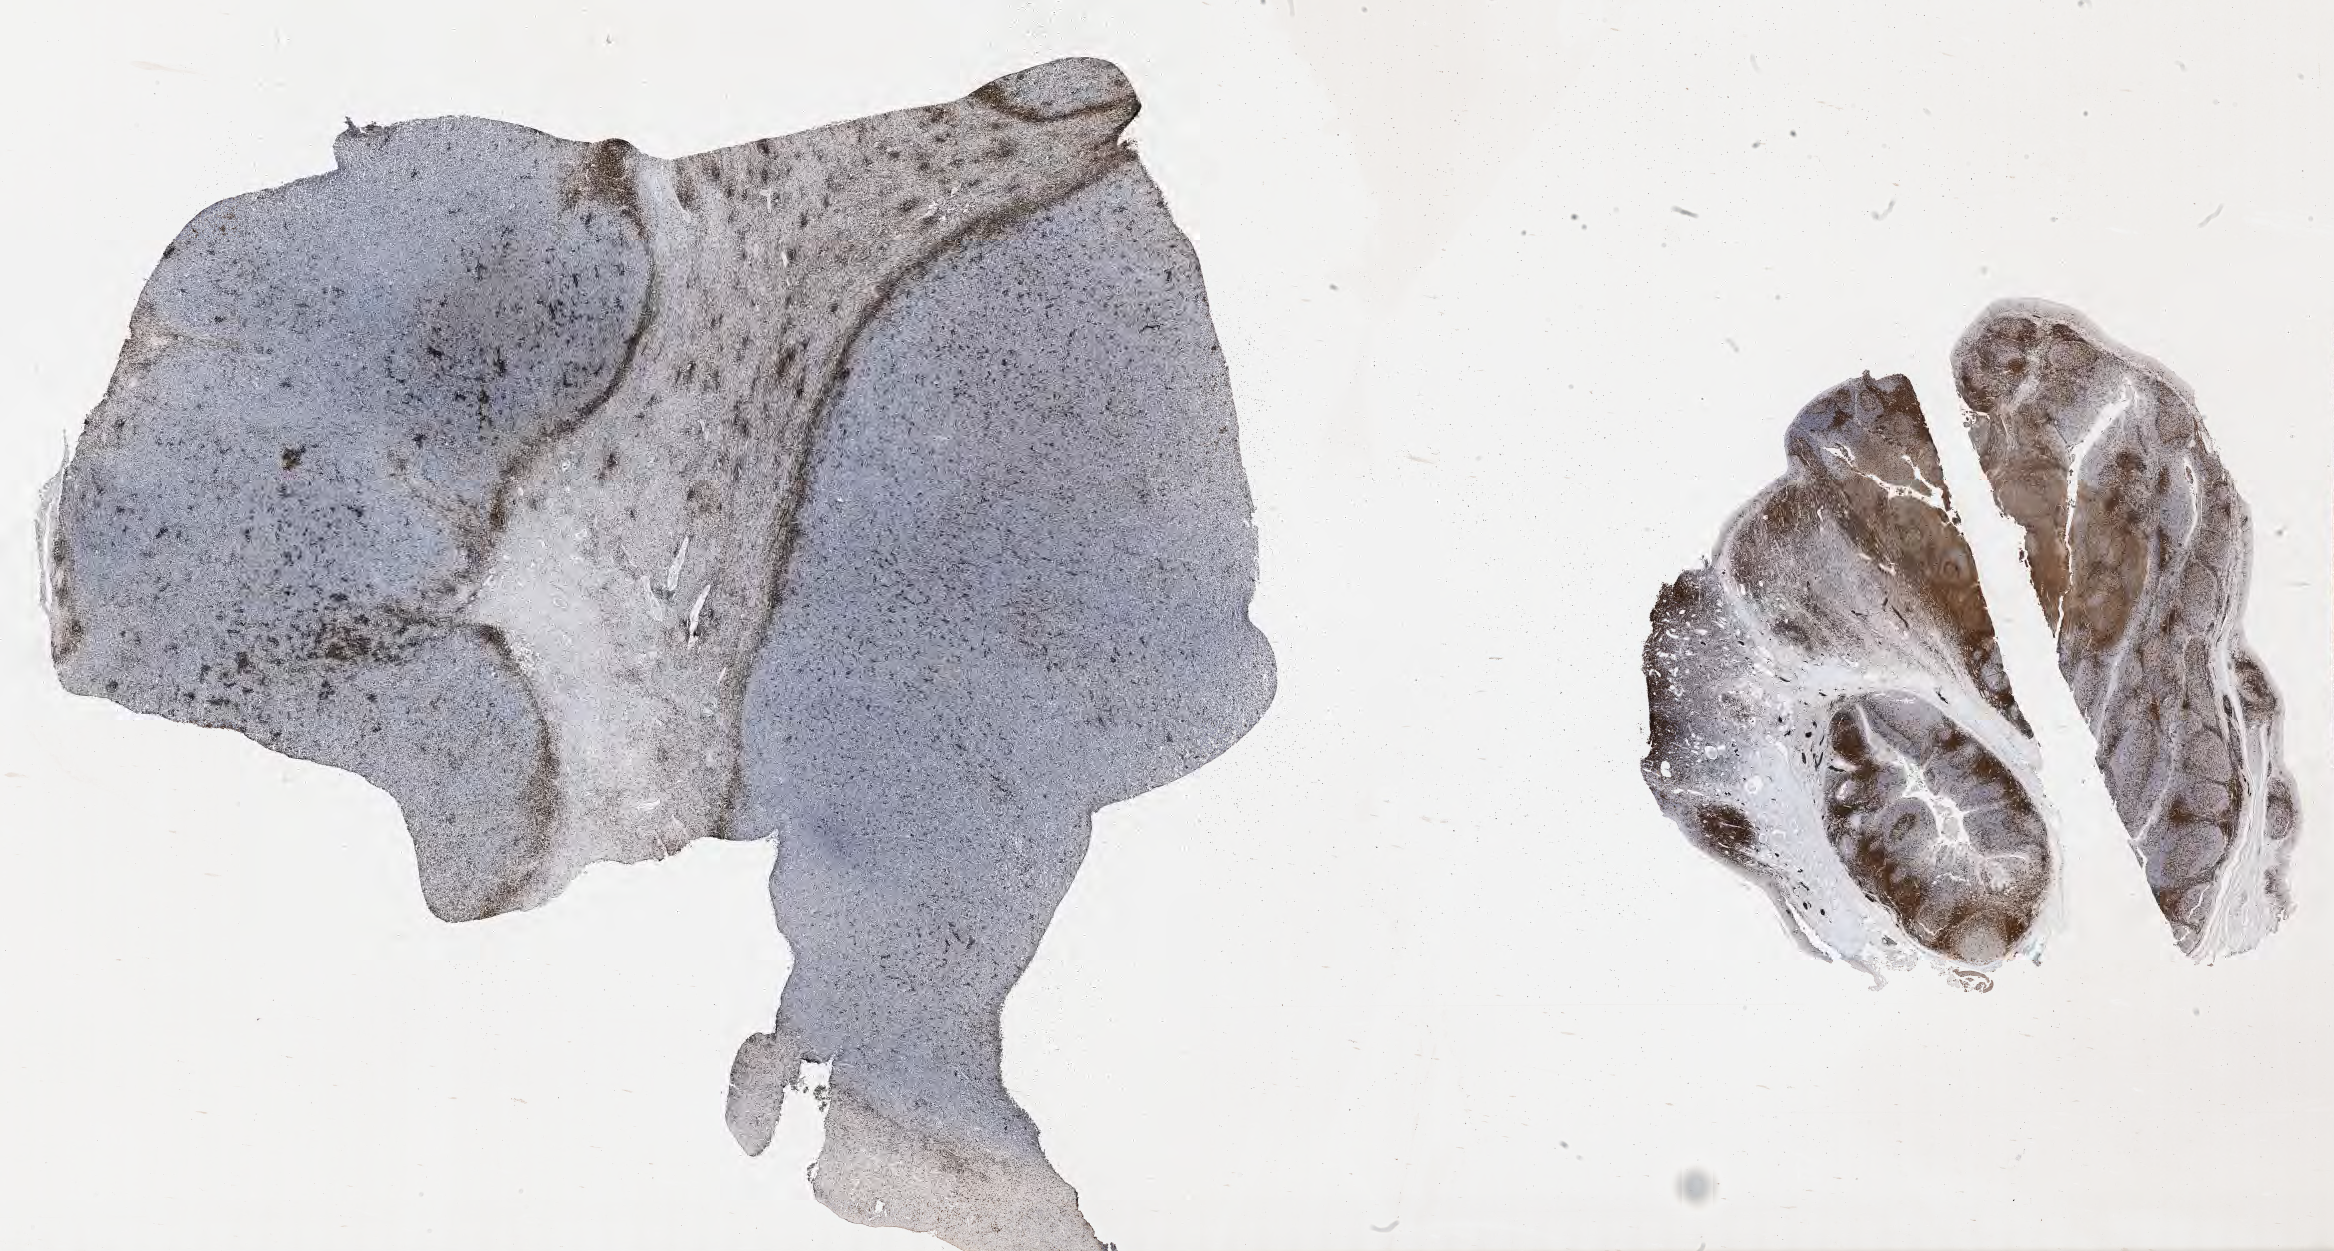
Whole-slide image, immunohistochemical stain for CD3, whole scanned area (about 37.7 x 20.2 mm) shown as a low-resolution overview, specimen: tumor tissue. Patient: female, age at initial diagnosis 8 years.
Diagnosis: Burkitt lymphoma, NOS.